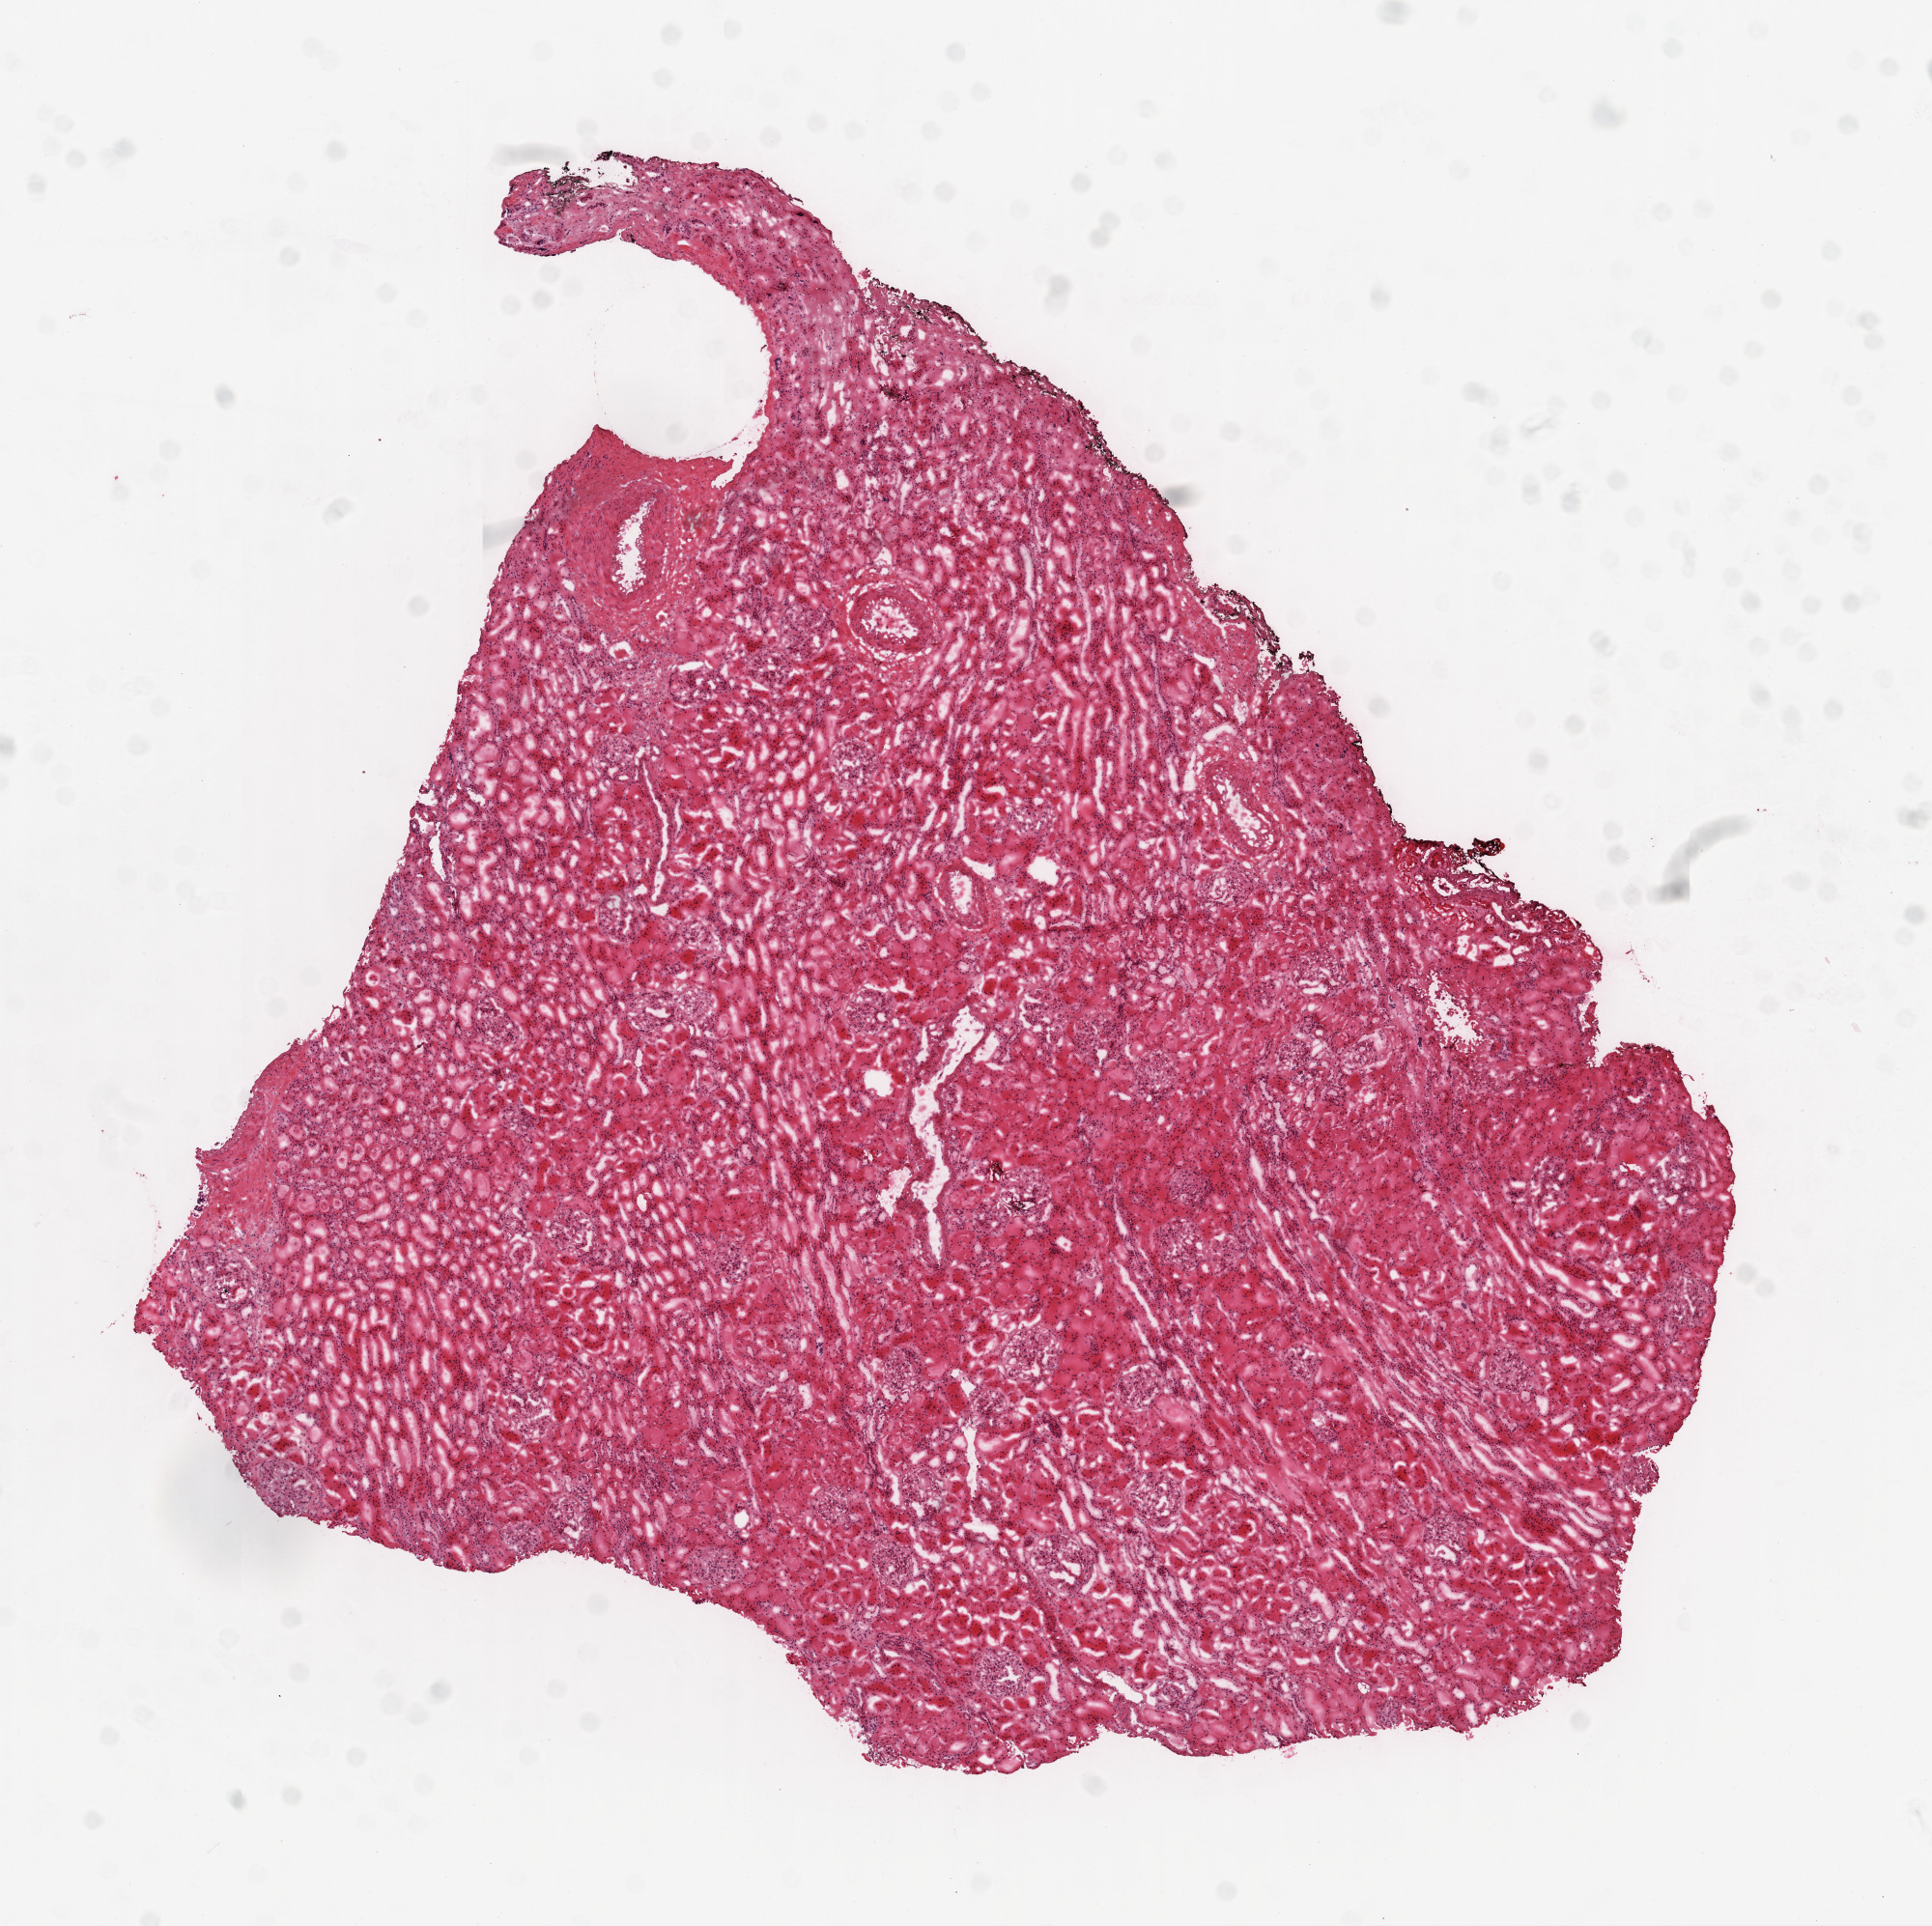
Digitized Hematoxylin and eosin (H&E) stained tissue section (whole slide), low-resolution overview of the scanned area, about 8.0 x 8.0 mm, frozen section from the top of the tissue portion, solid tissue normal (non-tumour tissue) sample from the kidney. Patient: male, age at initial diagnosis 57 years.
This section: solid tissue normal (non-tumour) sample from the same patient. Patient diagnosis: Clear cell adenocarcinoma, NOS.